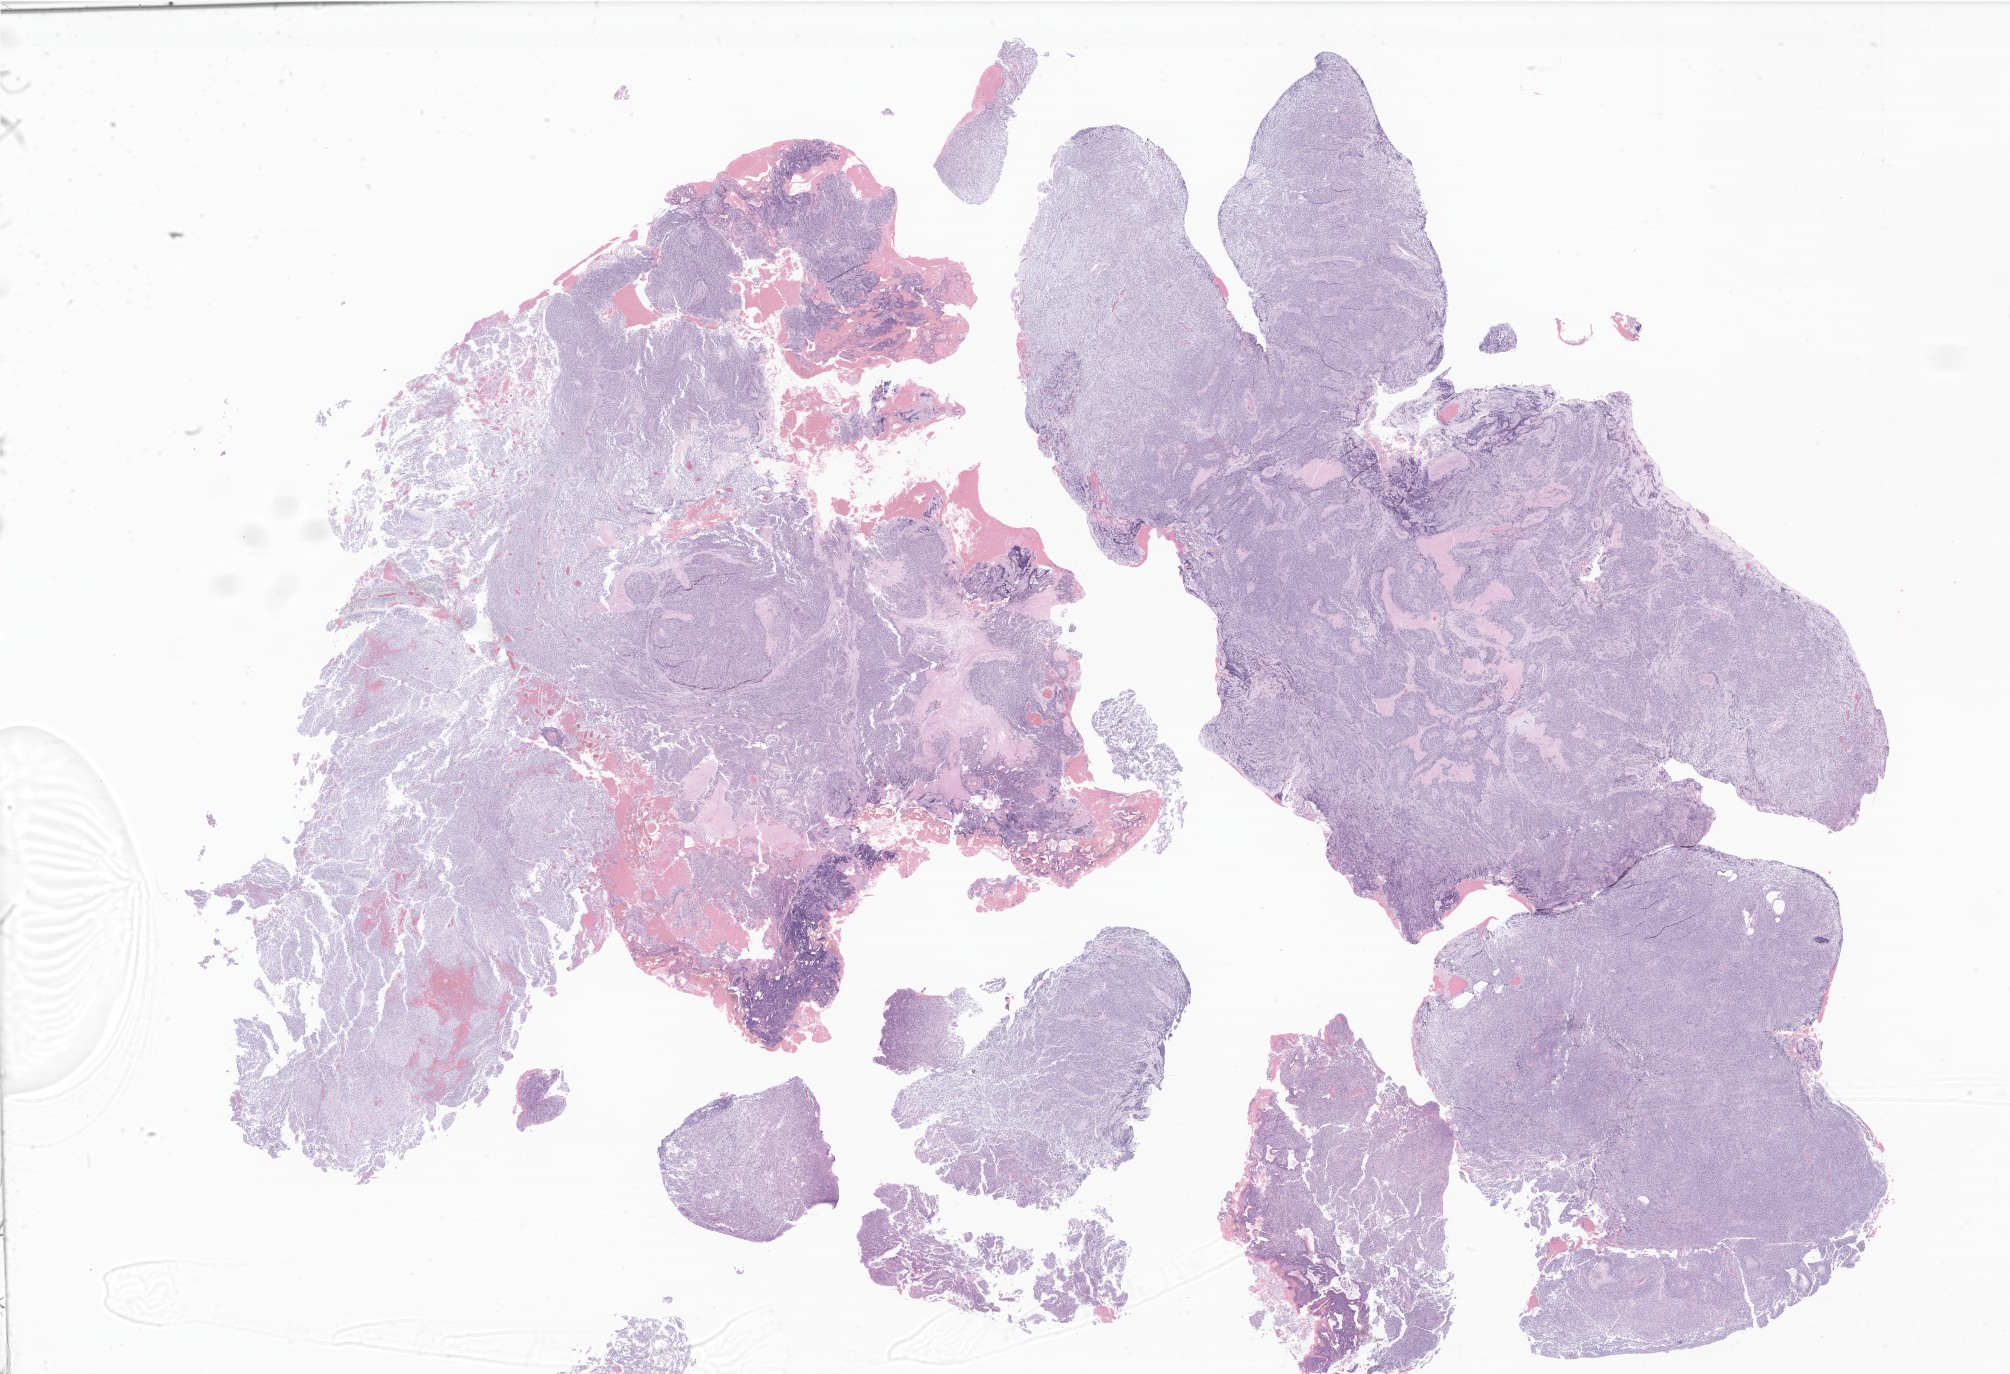
Hematoxylin and eosin (H&E) whole-slide image of tumor tissue from the brain, a low-resolution overview of the entire scanned area, about 33.9 x 23.2 mm; formalin-fixed paraffin-embedded section. Female patient, age 162 months (13 years 6 months).
Diagnosis (ICD-O-3 morphology term): Medulloblastoma, NOS.